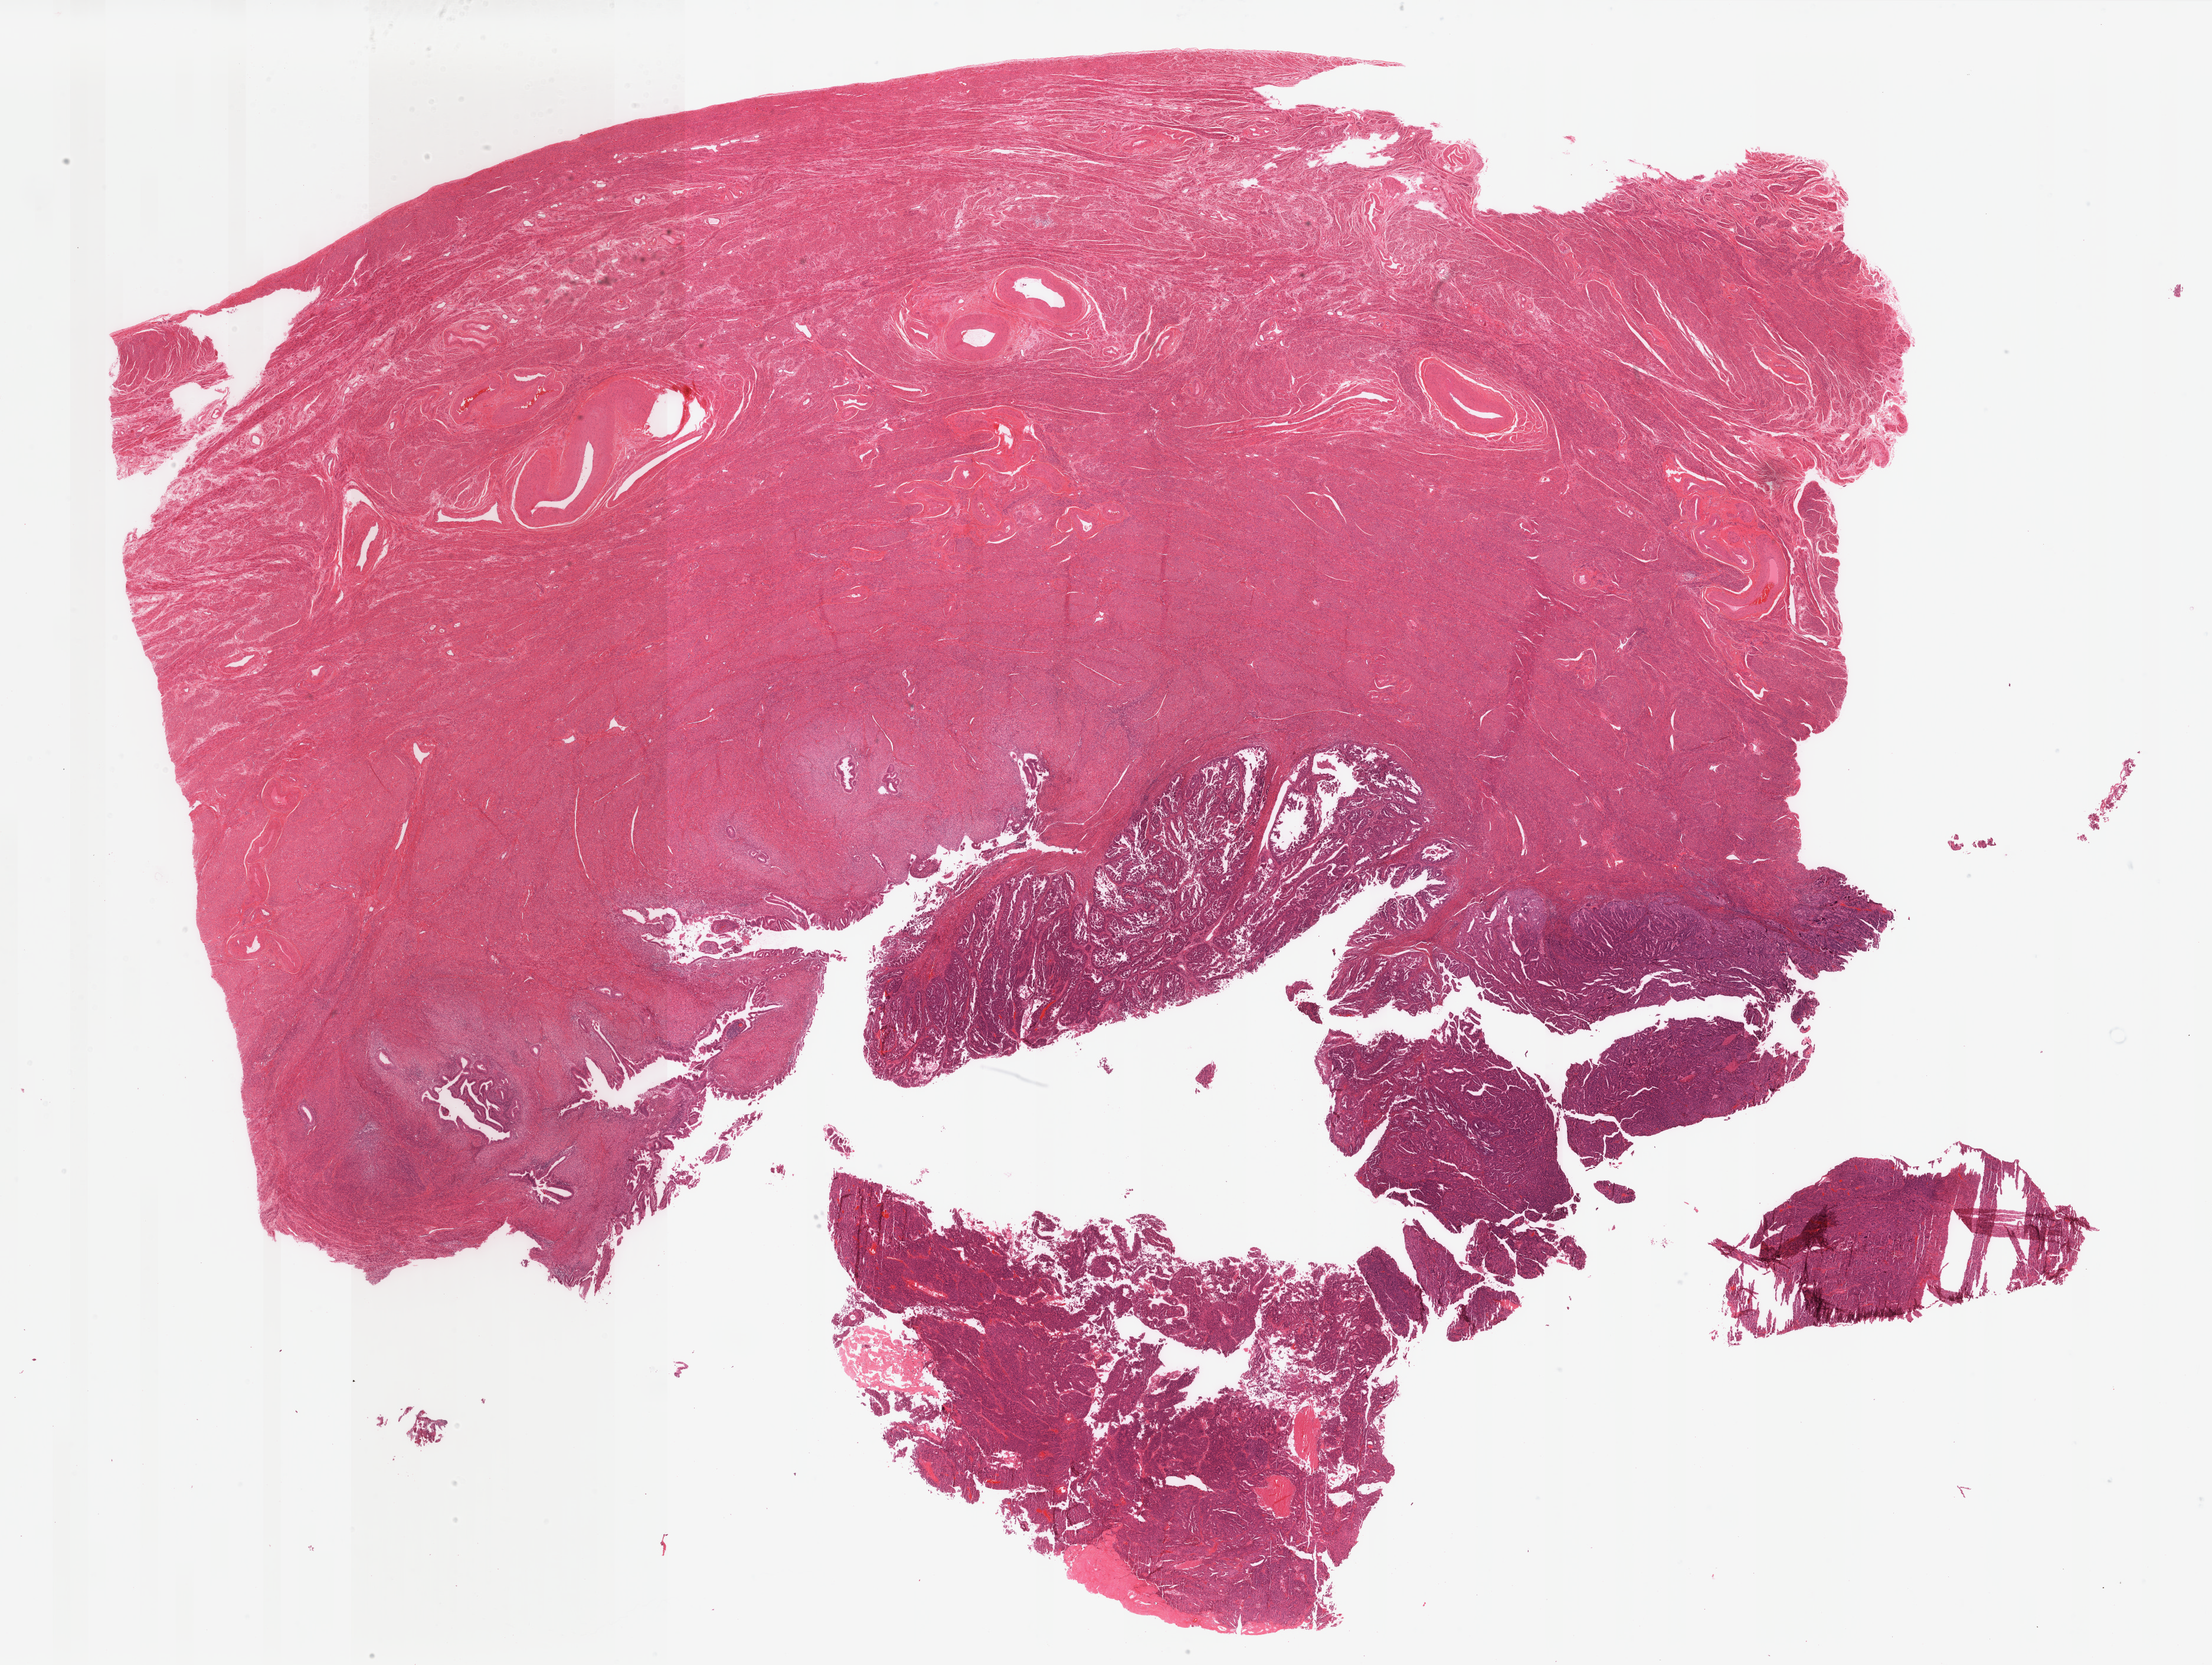
Hematoxylin and eosin (H&E) stained whole-slide image, whole scanned area (about 29.7 x 22.4 mm, acquisition: 40x scan) shown as a low-resolution overview. Formalin-fixed paraffin-embedded (FFPE) diagnostic section. Sample: primary tumour, uterus. Patient: female, age at initial diagnosis 68 years.
Histologic diagnosis: Serous cystadenocarcinoma, NOS (endometrium).